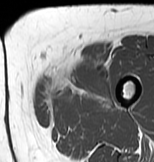
MRI of an extremity soft-tissue mass, one axial slice. Position 15 of 83 along the scan axis. MR volume resampled by the dataset authors to the PET/CT grid (not the native acquisition matrix). 154 × 162 image matrix, field of view 150 × 158 mm. Female patient. From the clinical record (not read from this slice): histological type: myxofibrosarcoma; grade: intermediate; site of the primary tumour: left thigh.
Structures marked on this image (expert contour drawn on MRI and transferred to this co-registered scan by the dataset authors):
- gross tumour volume including surrounding oedema: bounding box [x1, y1, x2, y2] px = [39, 64, 114, 110]
- gross tumour volume (mass): [55, 64, 100, 90]